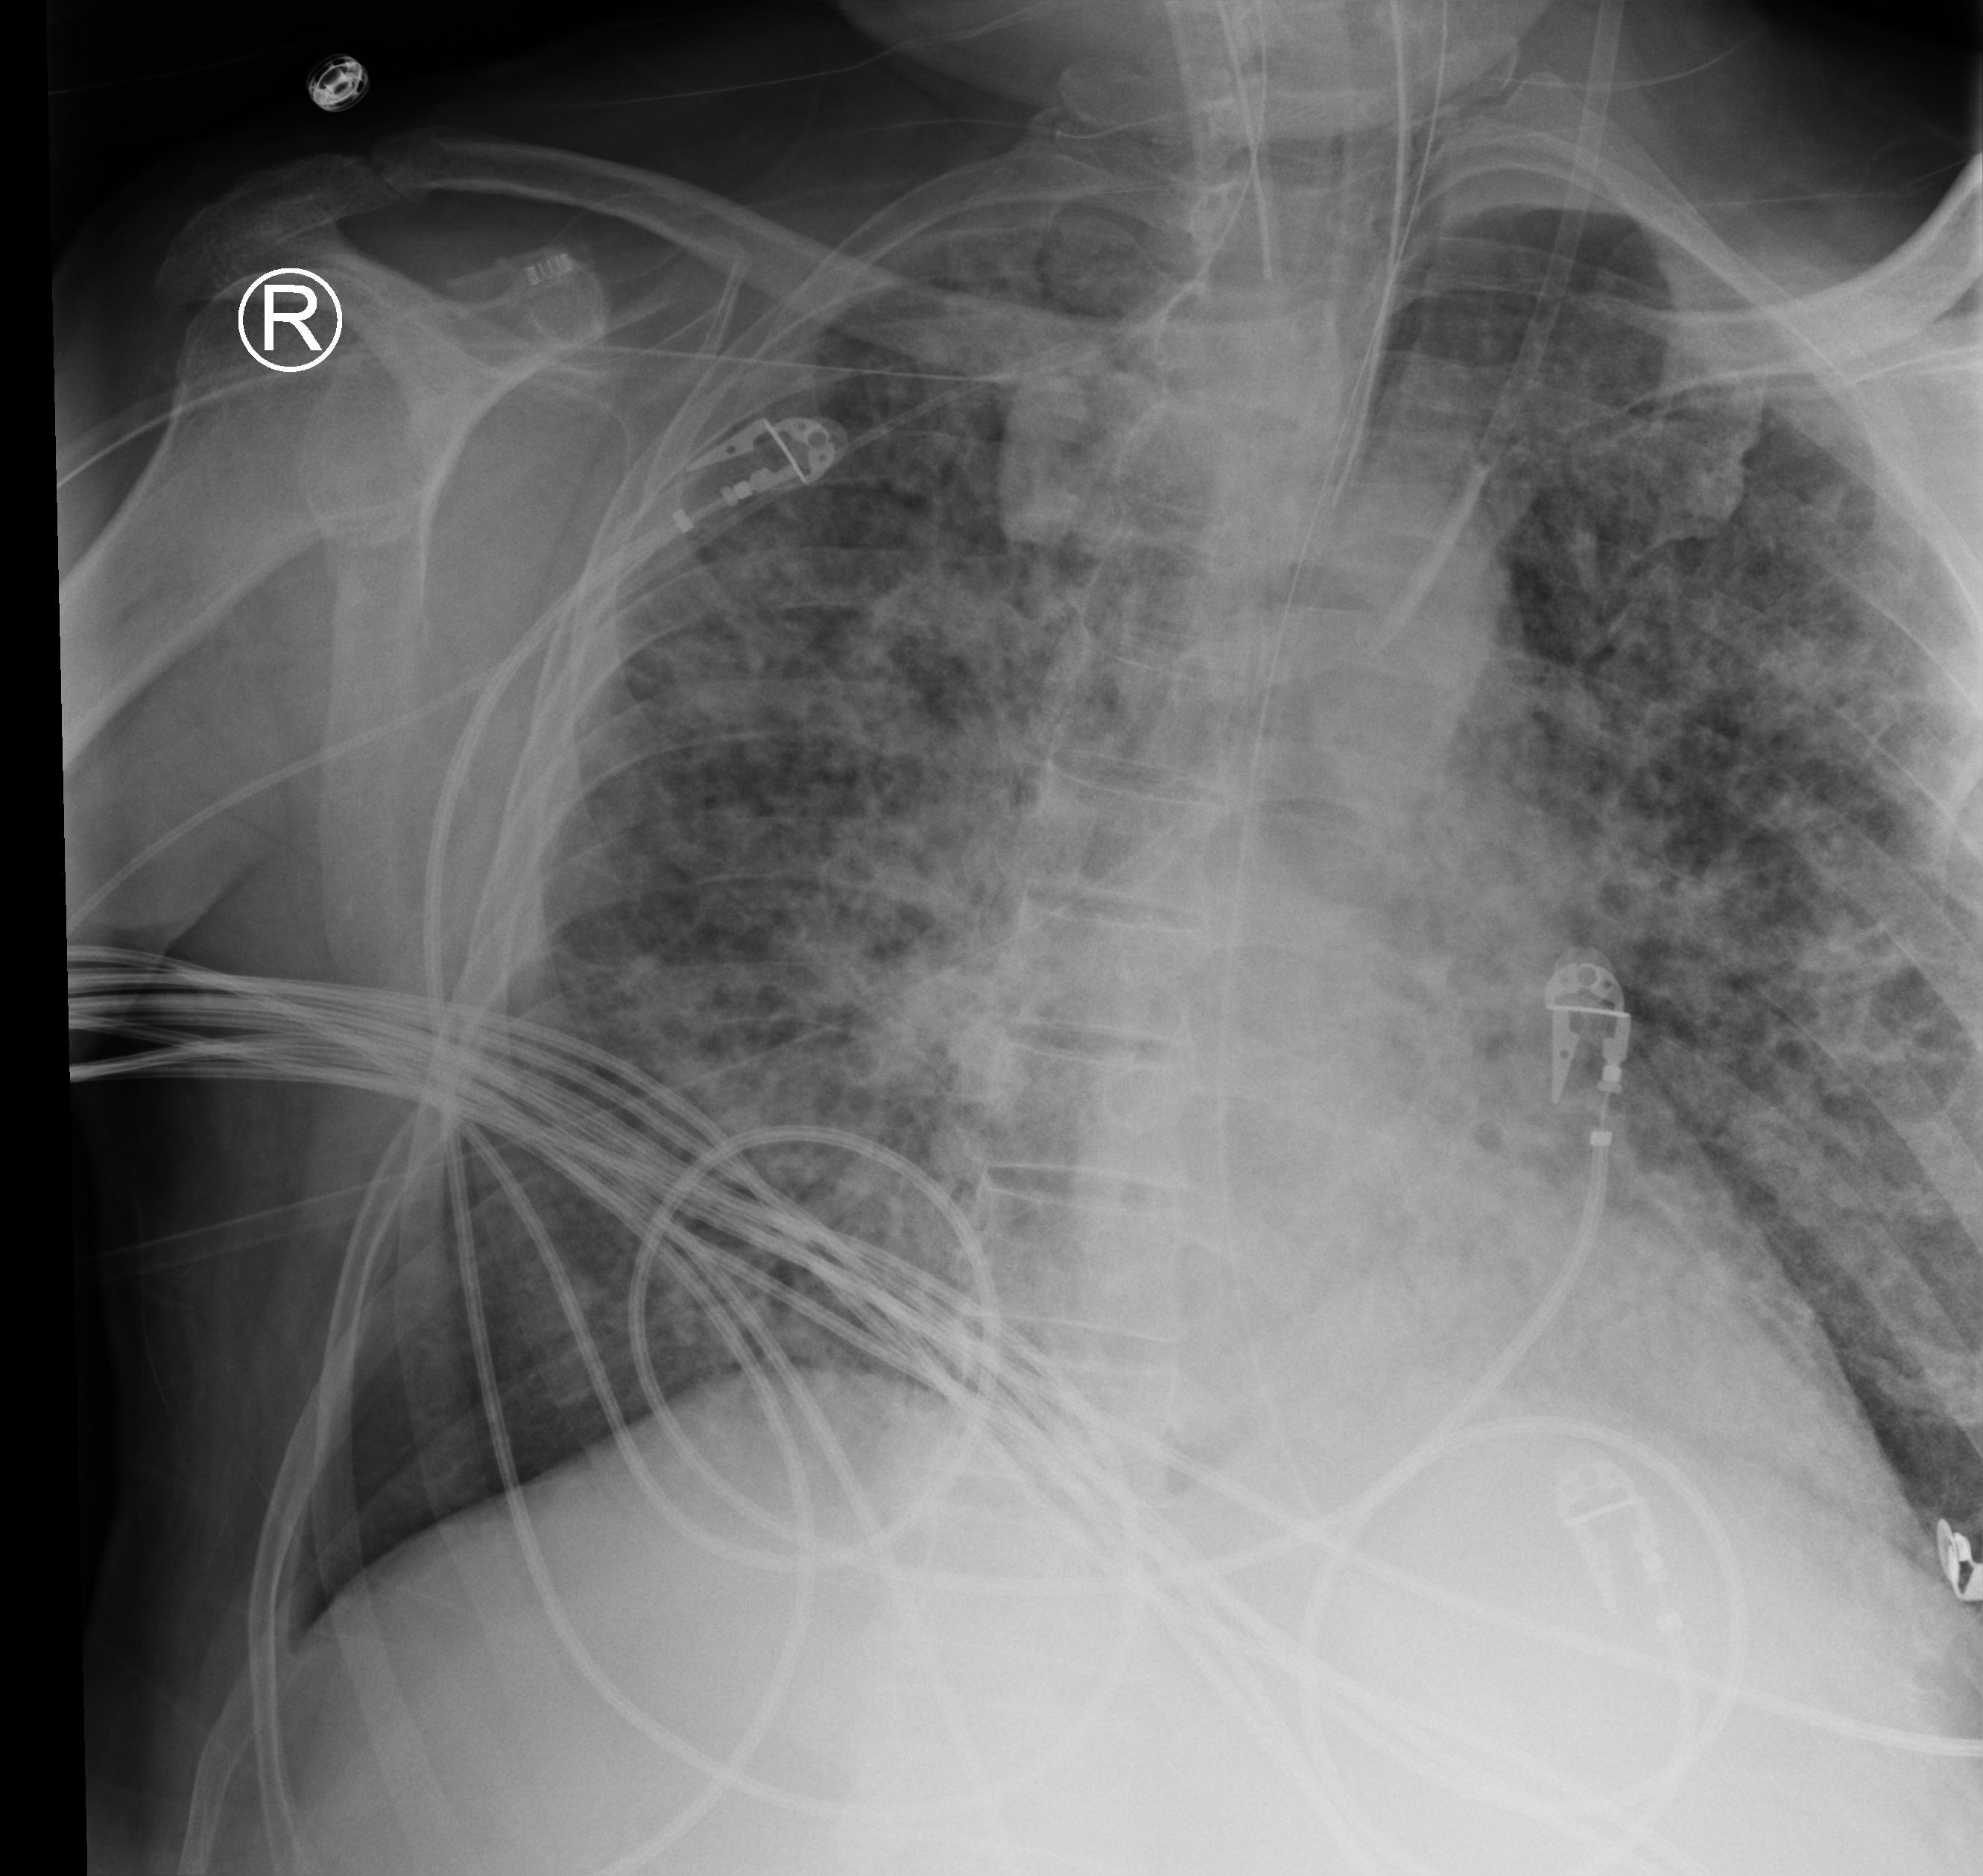
Portable chest radiograph, anteroposterior (AP) projection. Patient hospitalised with COVID-19; male, aged 60–74 years.
Hospital-stay facts (about this admission, not read from this image; timing relative to this image not recorded): mechanically ventilated during this hospital stay: yes.